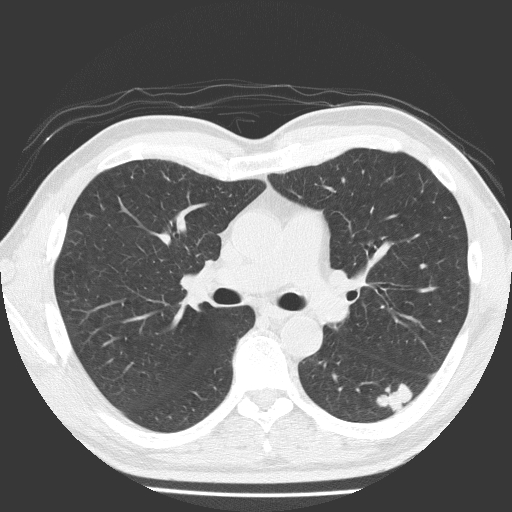
Axial slice from a low-dose chest CT screening exam, first (baseline) screen, lung window (W 1500 / L -600 HU), lung (sharp) reconstruction kernel (FC51), 120 kVp. Male participant, aged 58 years at enrolment. Current smoker at enrolment.
Lesion marked by an expert reader, bounding box [x1, y1, x2, y2] px = [369, 374, 425, 423]. The screening reader recorded 4 non-calcified nodules or masses ≥4 mm on this exam (left lower lobe, left lower lobe, right middle lobe, left upper lobe); which of them this box marks is not recorded. Official screen result: positive, change unspecified: nodule(s) >= 4 mm or enlarging nodule(s), mass(es), or other non-specific abnormalities suspicious for lung cancer.